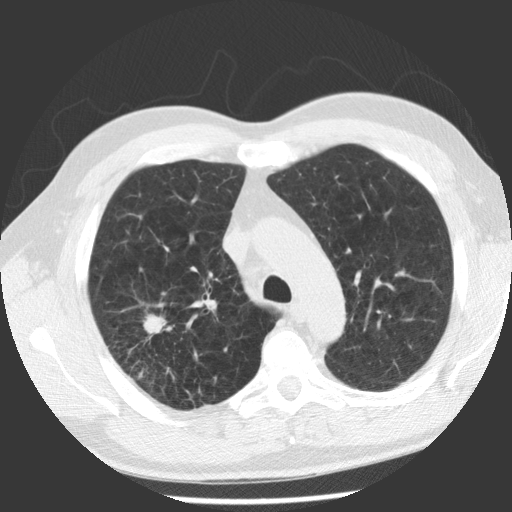
Low-dose screening chest CT, one axial slice. Slice 83 of 112 in the series (ordered by position). 140 kVp. Lung window (W 1500 / L -600 HU). 512 × 512 image matrix, field of view 344 × 344 mm.
Outlined on this slice (manually delineated by an expert):
- lesion 1 (tumor, upper lobe of right lung): bounding box (x1, y1, x2, y2) in pixels: (143, 314, 166, 335)